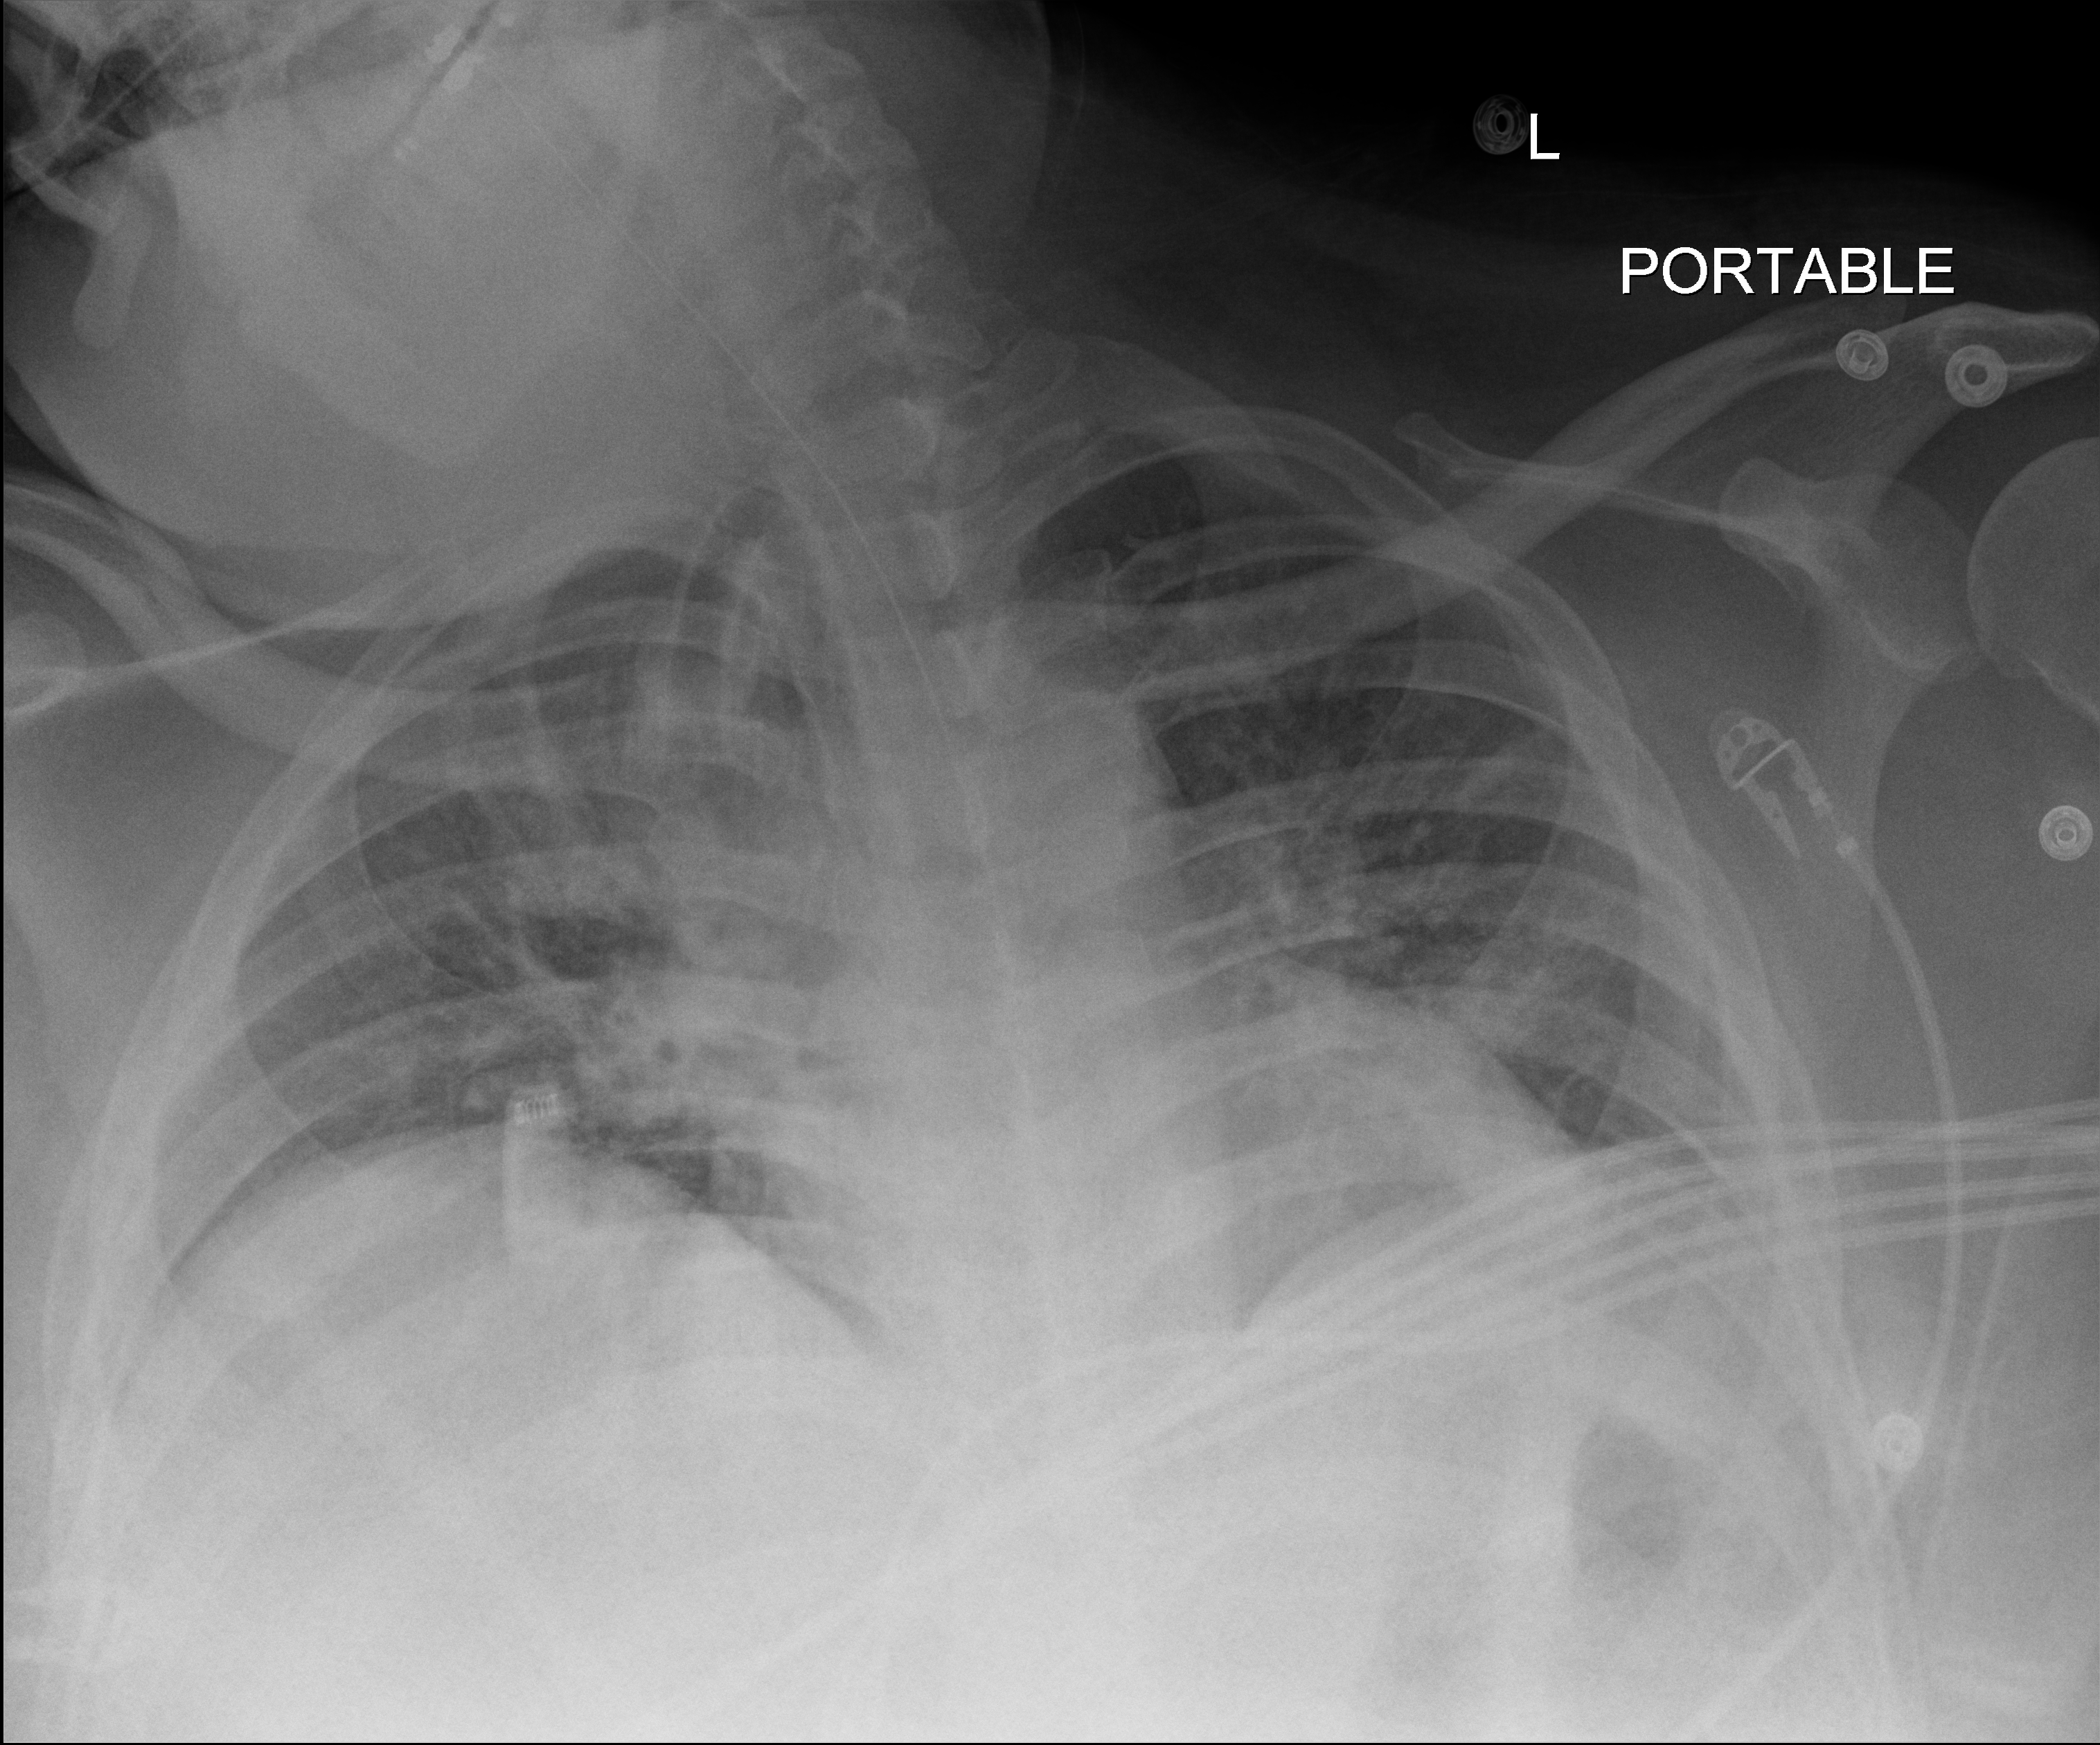
Portable chest radiograph; anteroposterior (AP) projection. Male patient hospitalised with COVID-19, age 18–59 years.
Admission-level facts for this patient (not findings on this image; timing relative to this image not recorded): admitted to intensive care during this hospital stay: yes; chronic kidney disease (admission record): no.